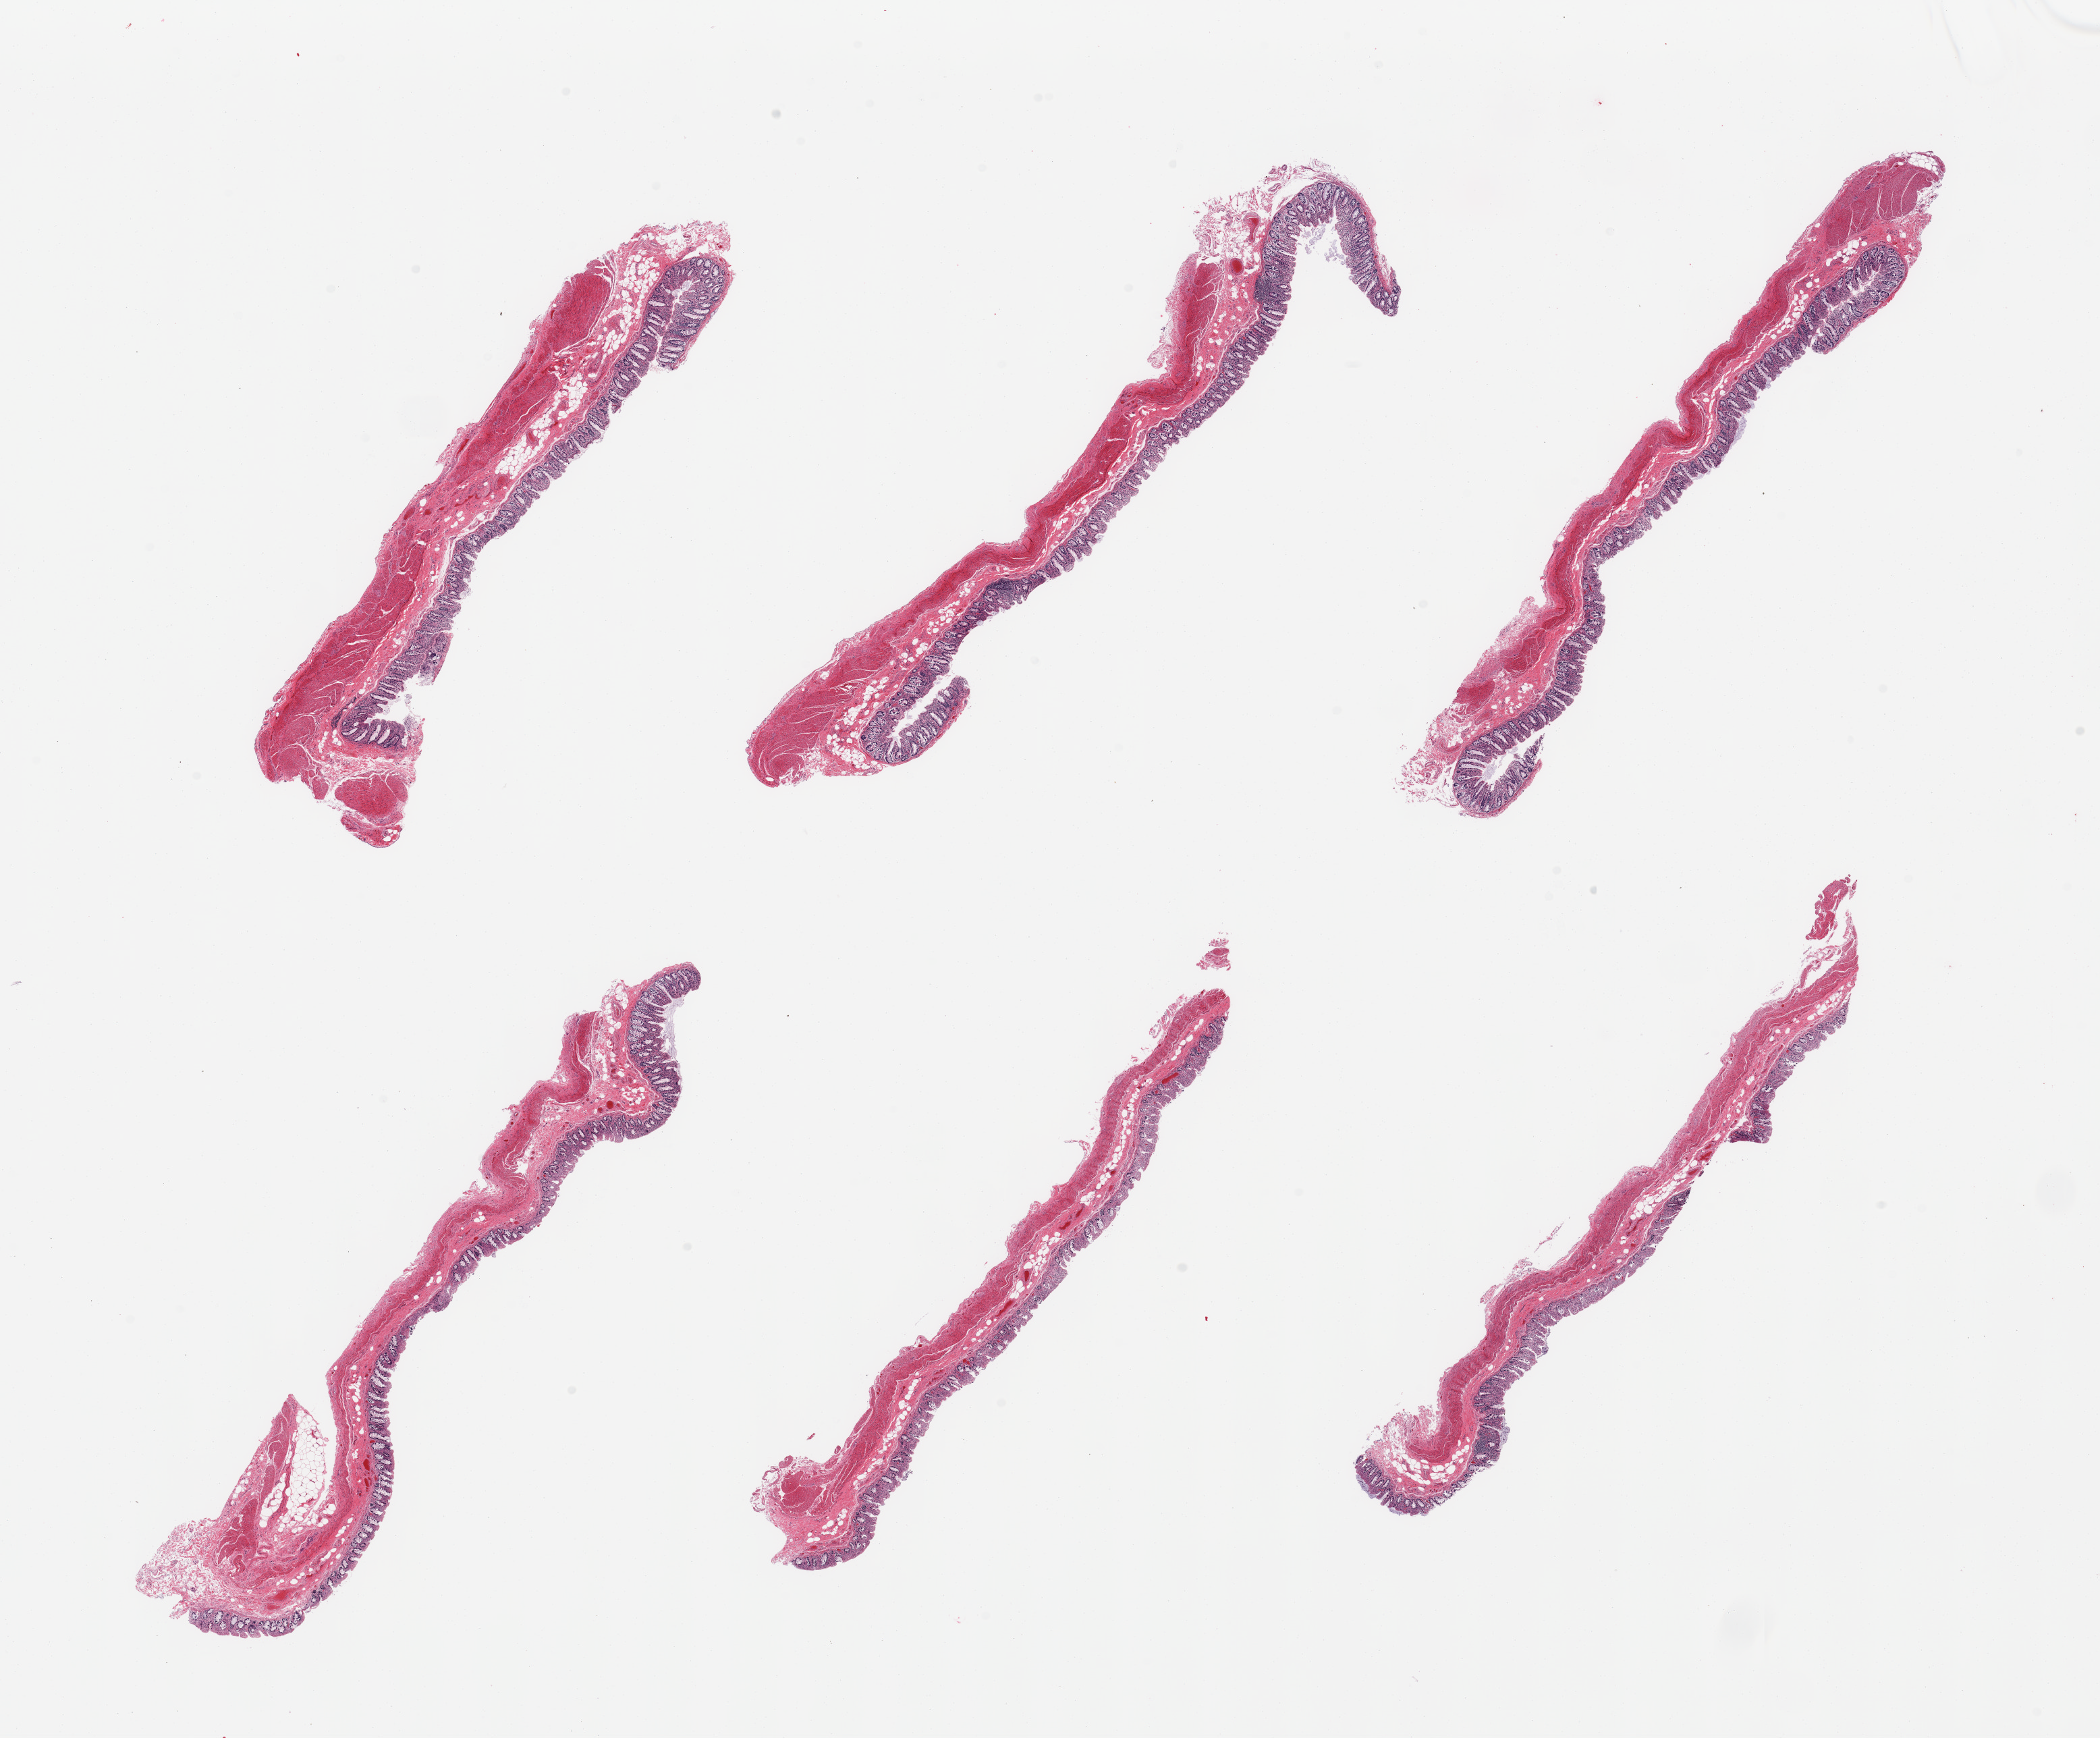
Haematoxylin and eosin whole-slide image, low-resolution overview of the scanned area, about 24.6 x 20.4 mm (slide scanned at 20x); PAXgene-fixed paraffin-embedded (PFPE) section; section of transverse colon (target tissue); tissue donor sample. Donor: male.
* reviewer comment on this tissue sample: 6 pieces, mucosa is ~0.3mm, ~40-50% thickness